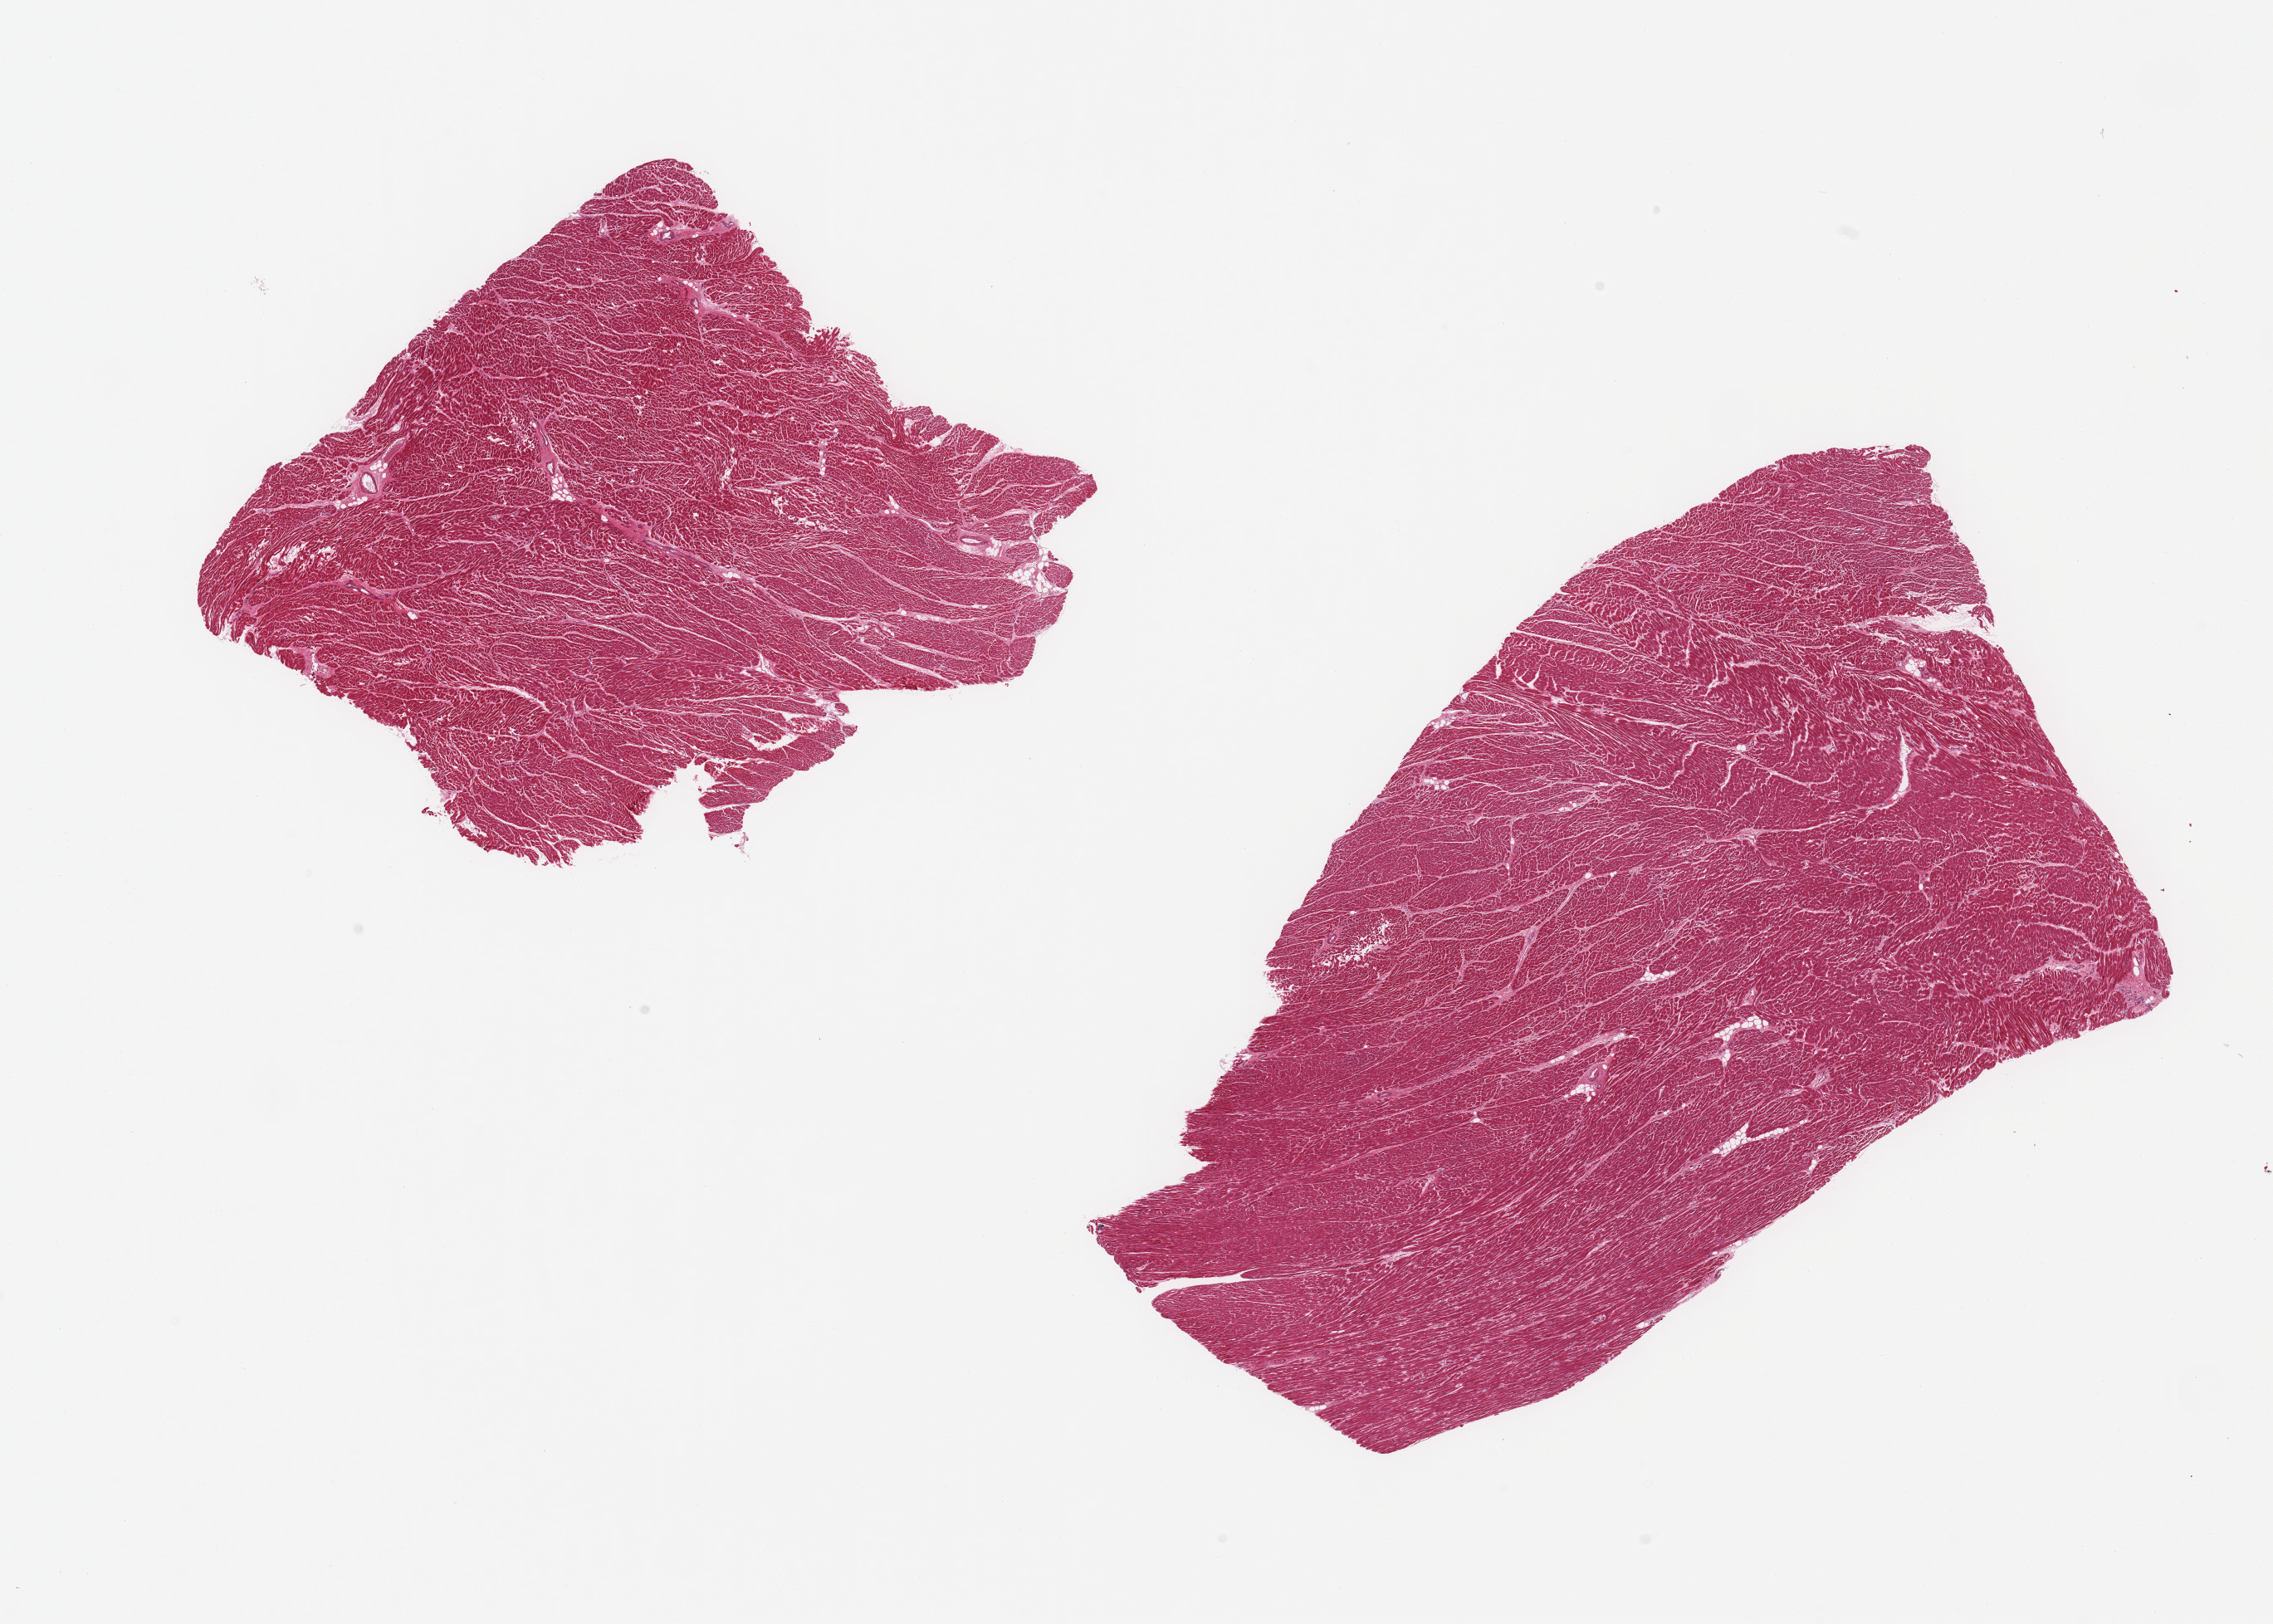
Digitized haematoxylin and eosin-stained section, low-resolution overview of the scanned area, about 21.7 x 15.5 mm, PAXgene-fixed paraffin-embedded (PFPE) section, section of heart (target tissue), donor tissue sample. Donor: male.
Pathologist's review note for this sample: 2 pieces; mild interstitial fibrosis; fatty streaks consistent with fatty degeneration.